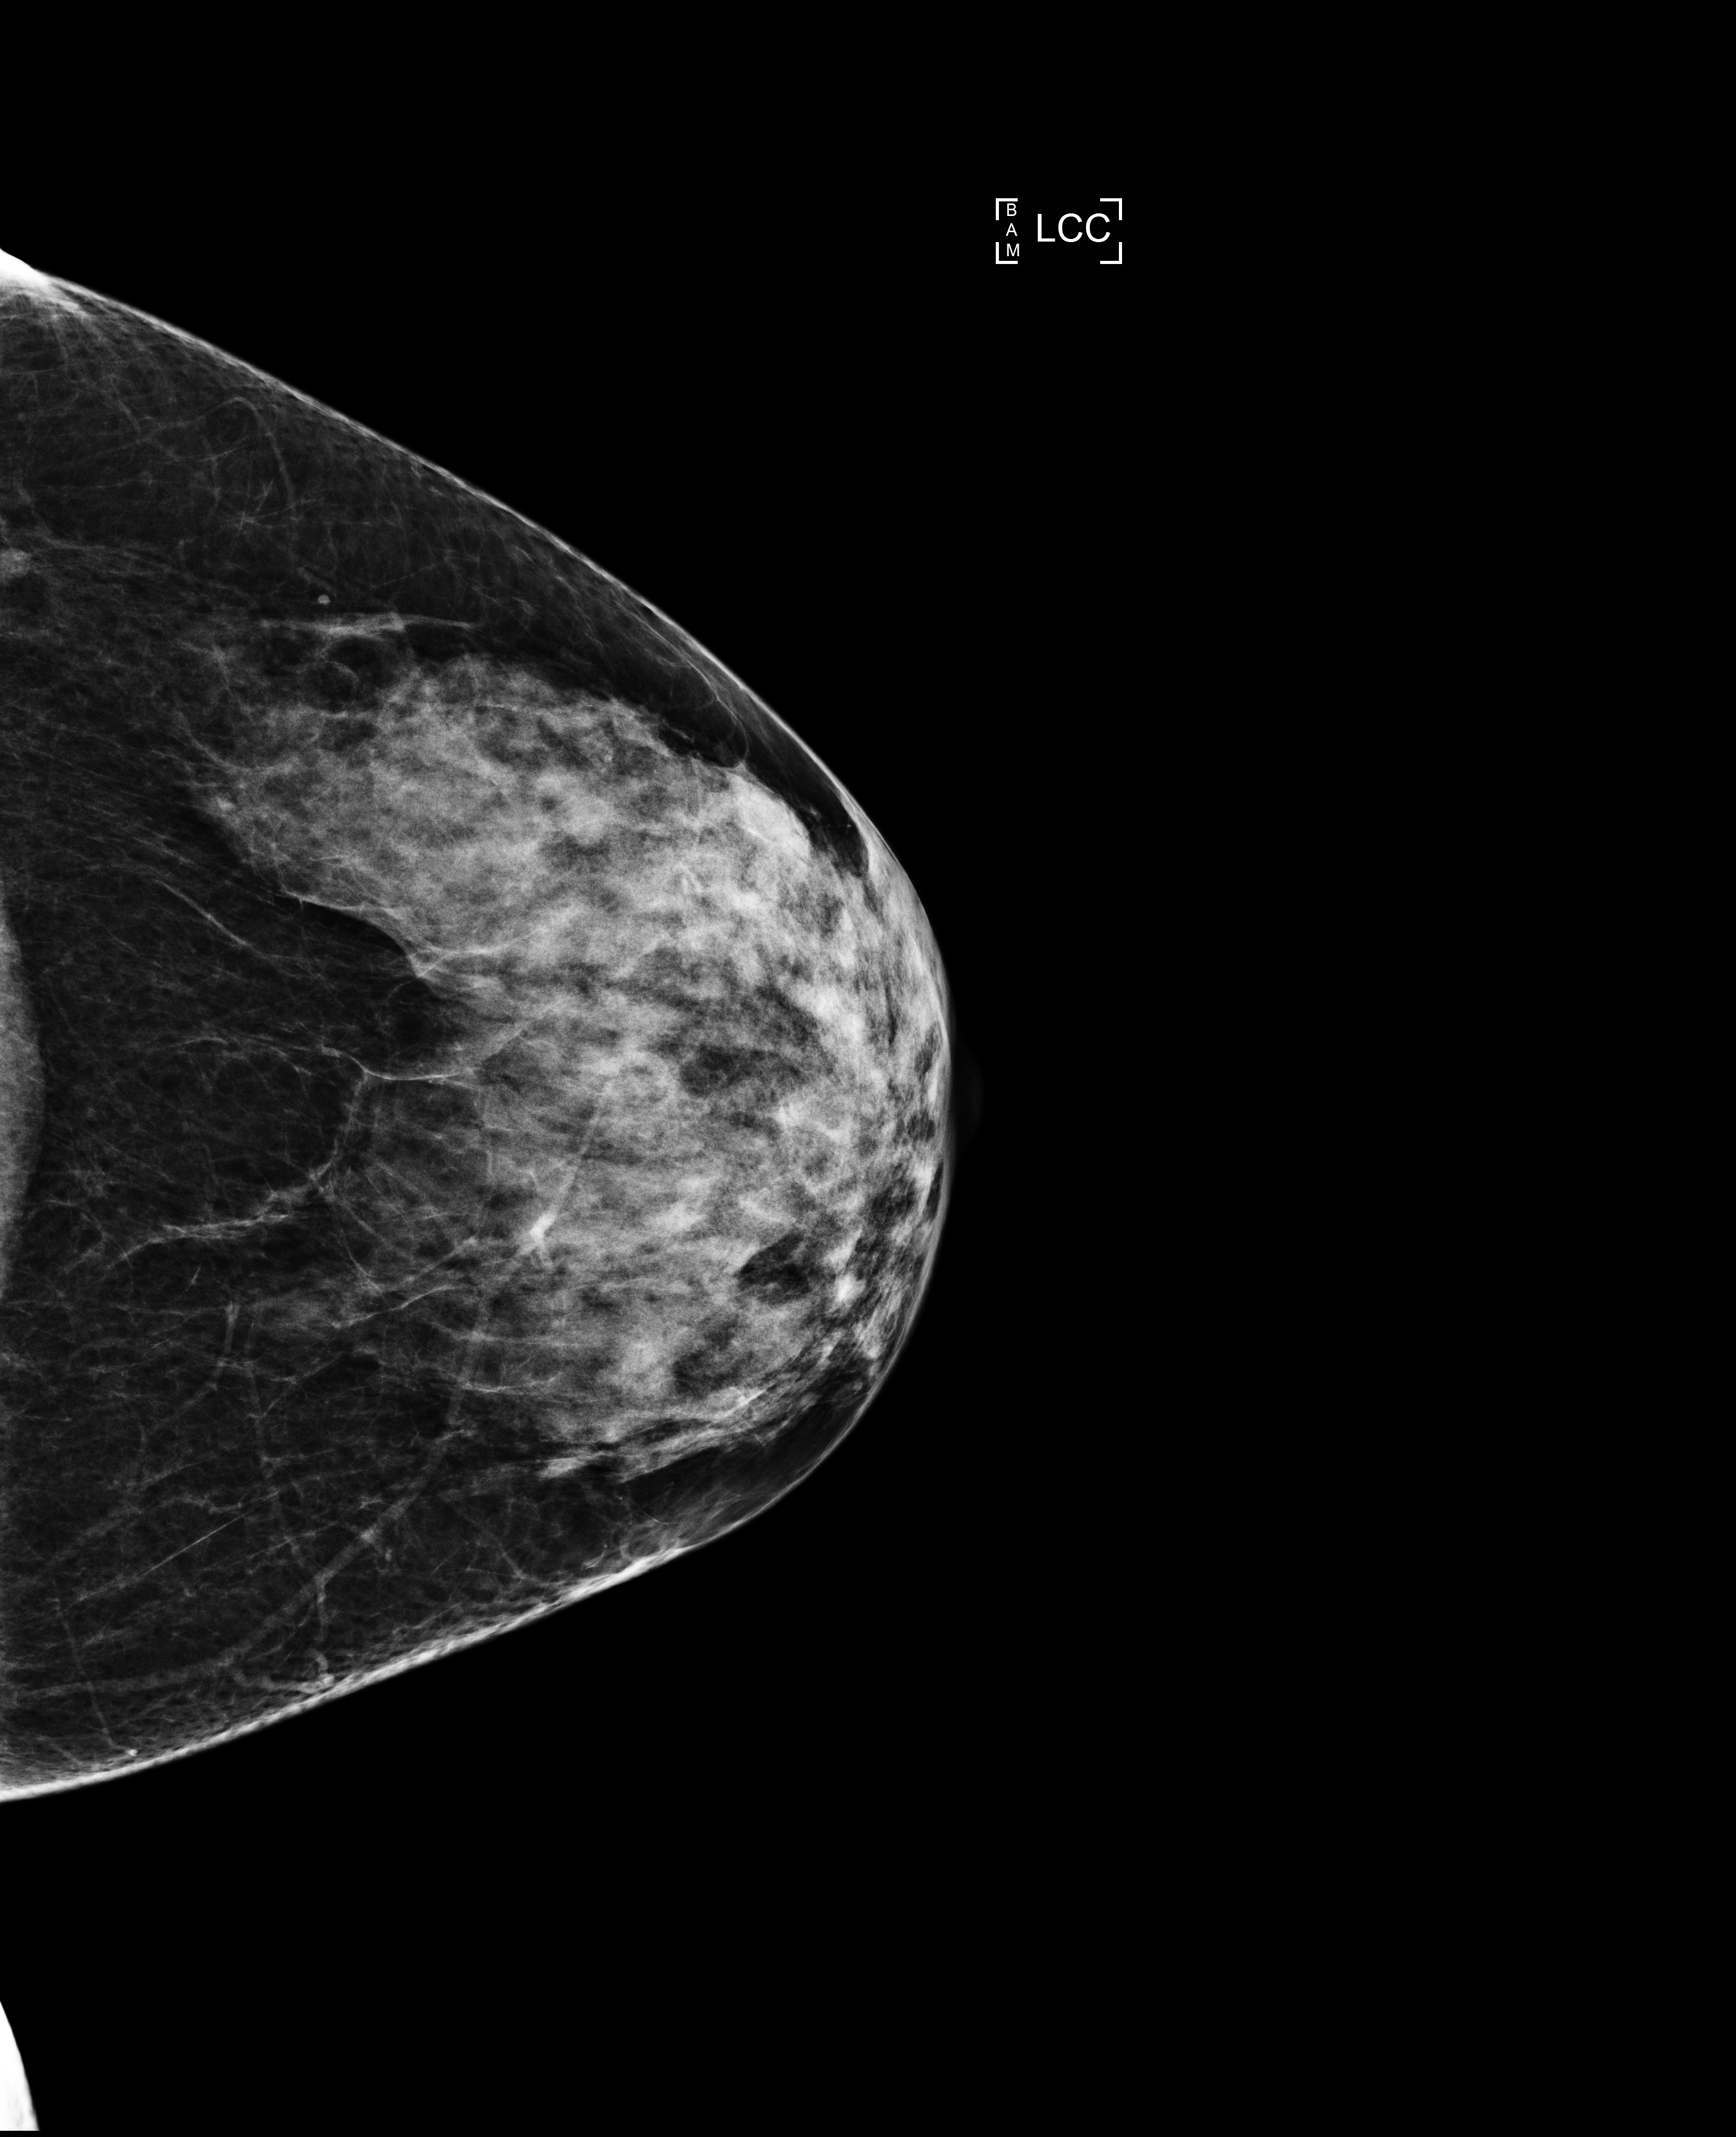
Annual screening mammography examination, compressed breast thickness 45 mm. Patient: female, 55 years.
Image type: full-field digital mammogram. Breast: left. Projection: craniocaudal (CC) view.